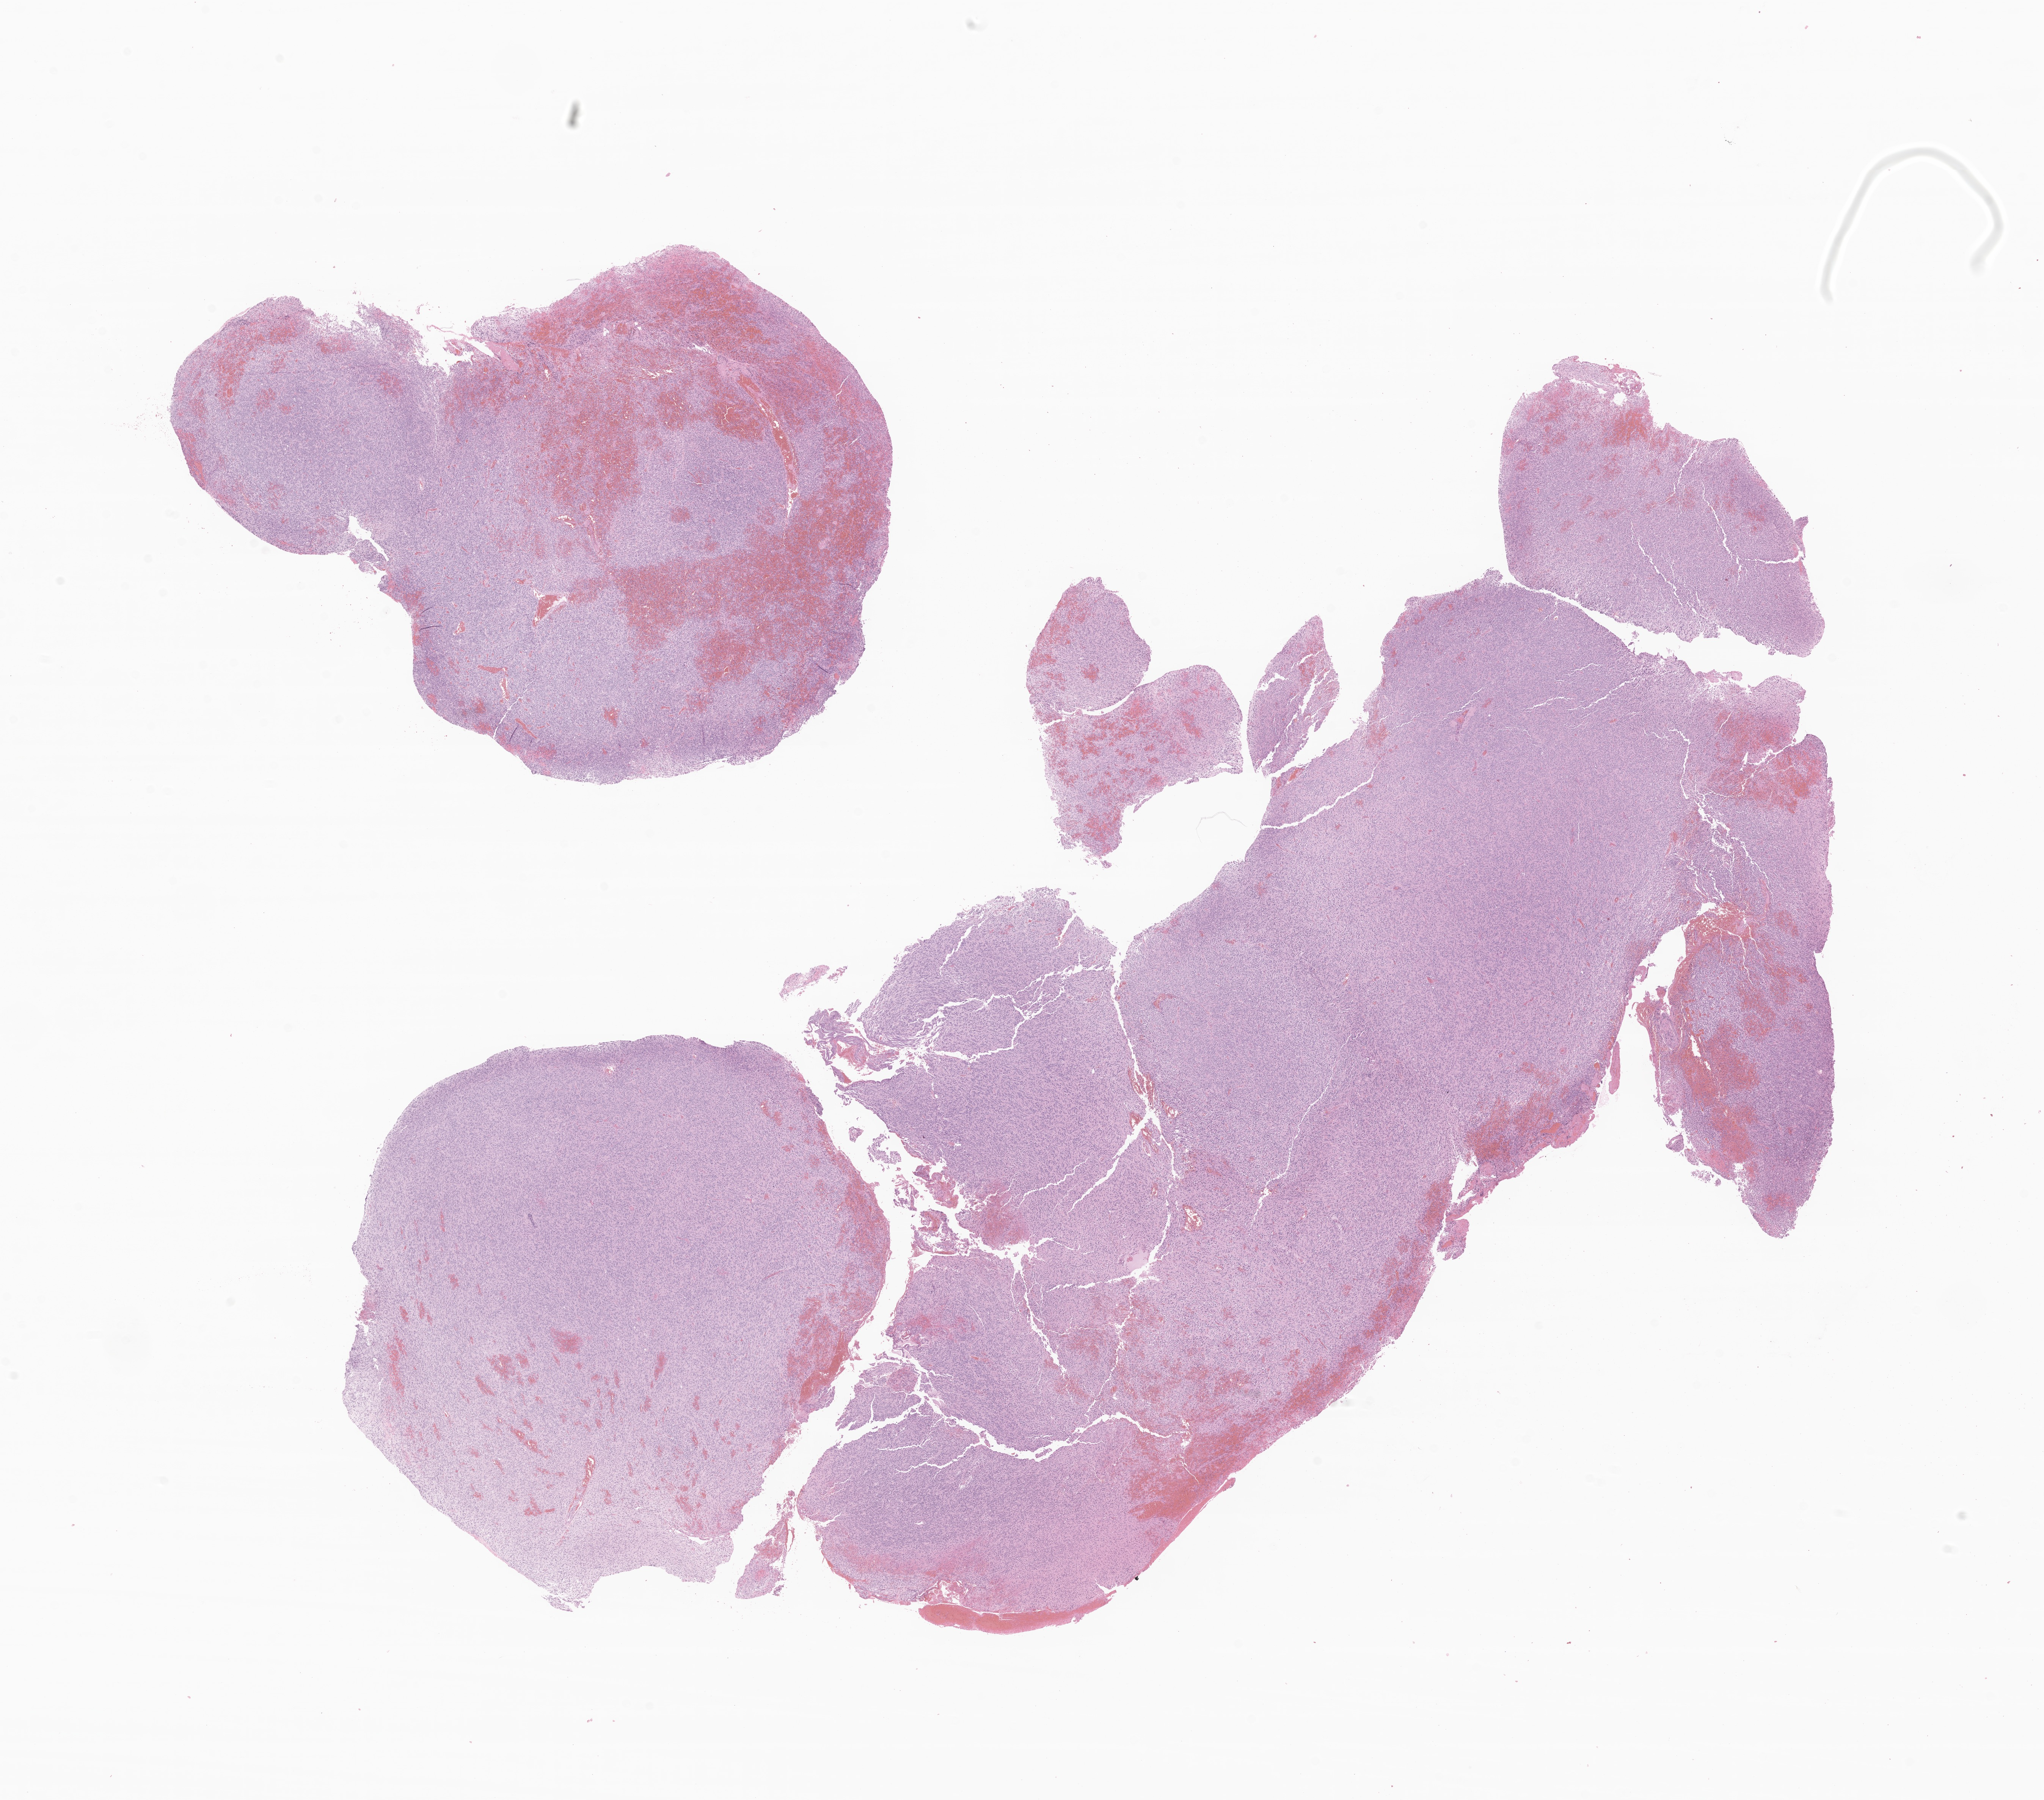
Whole-slide image, H&E stain of tumor tissue from the brain, shown as a low-resolution overview of the whole scanned area (about 22.7 x 20.0 mm), FFPE section. Male patient, age 121 months (10 years 1 month).
Recorded diagnosis: Glioma, malignant.